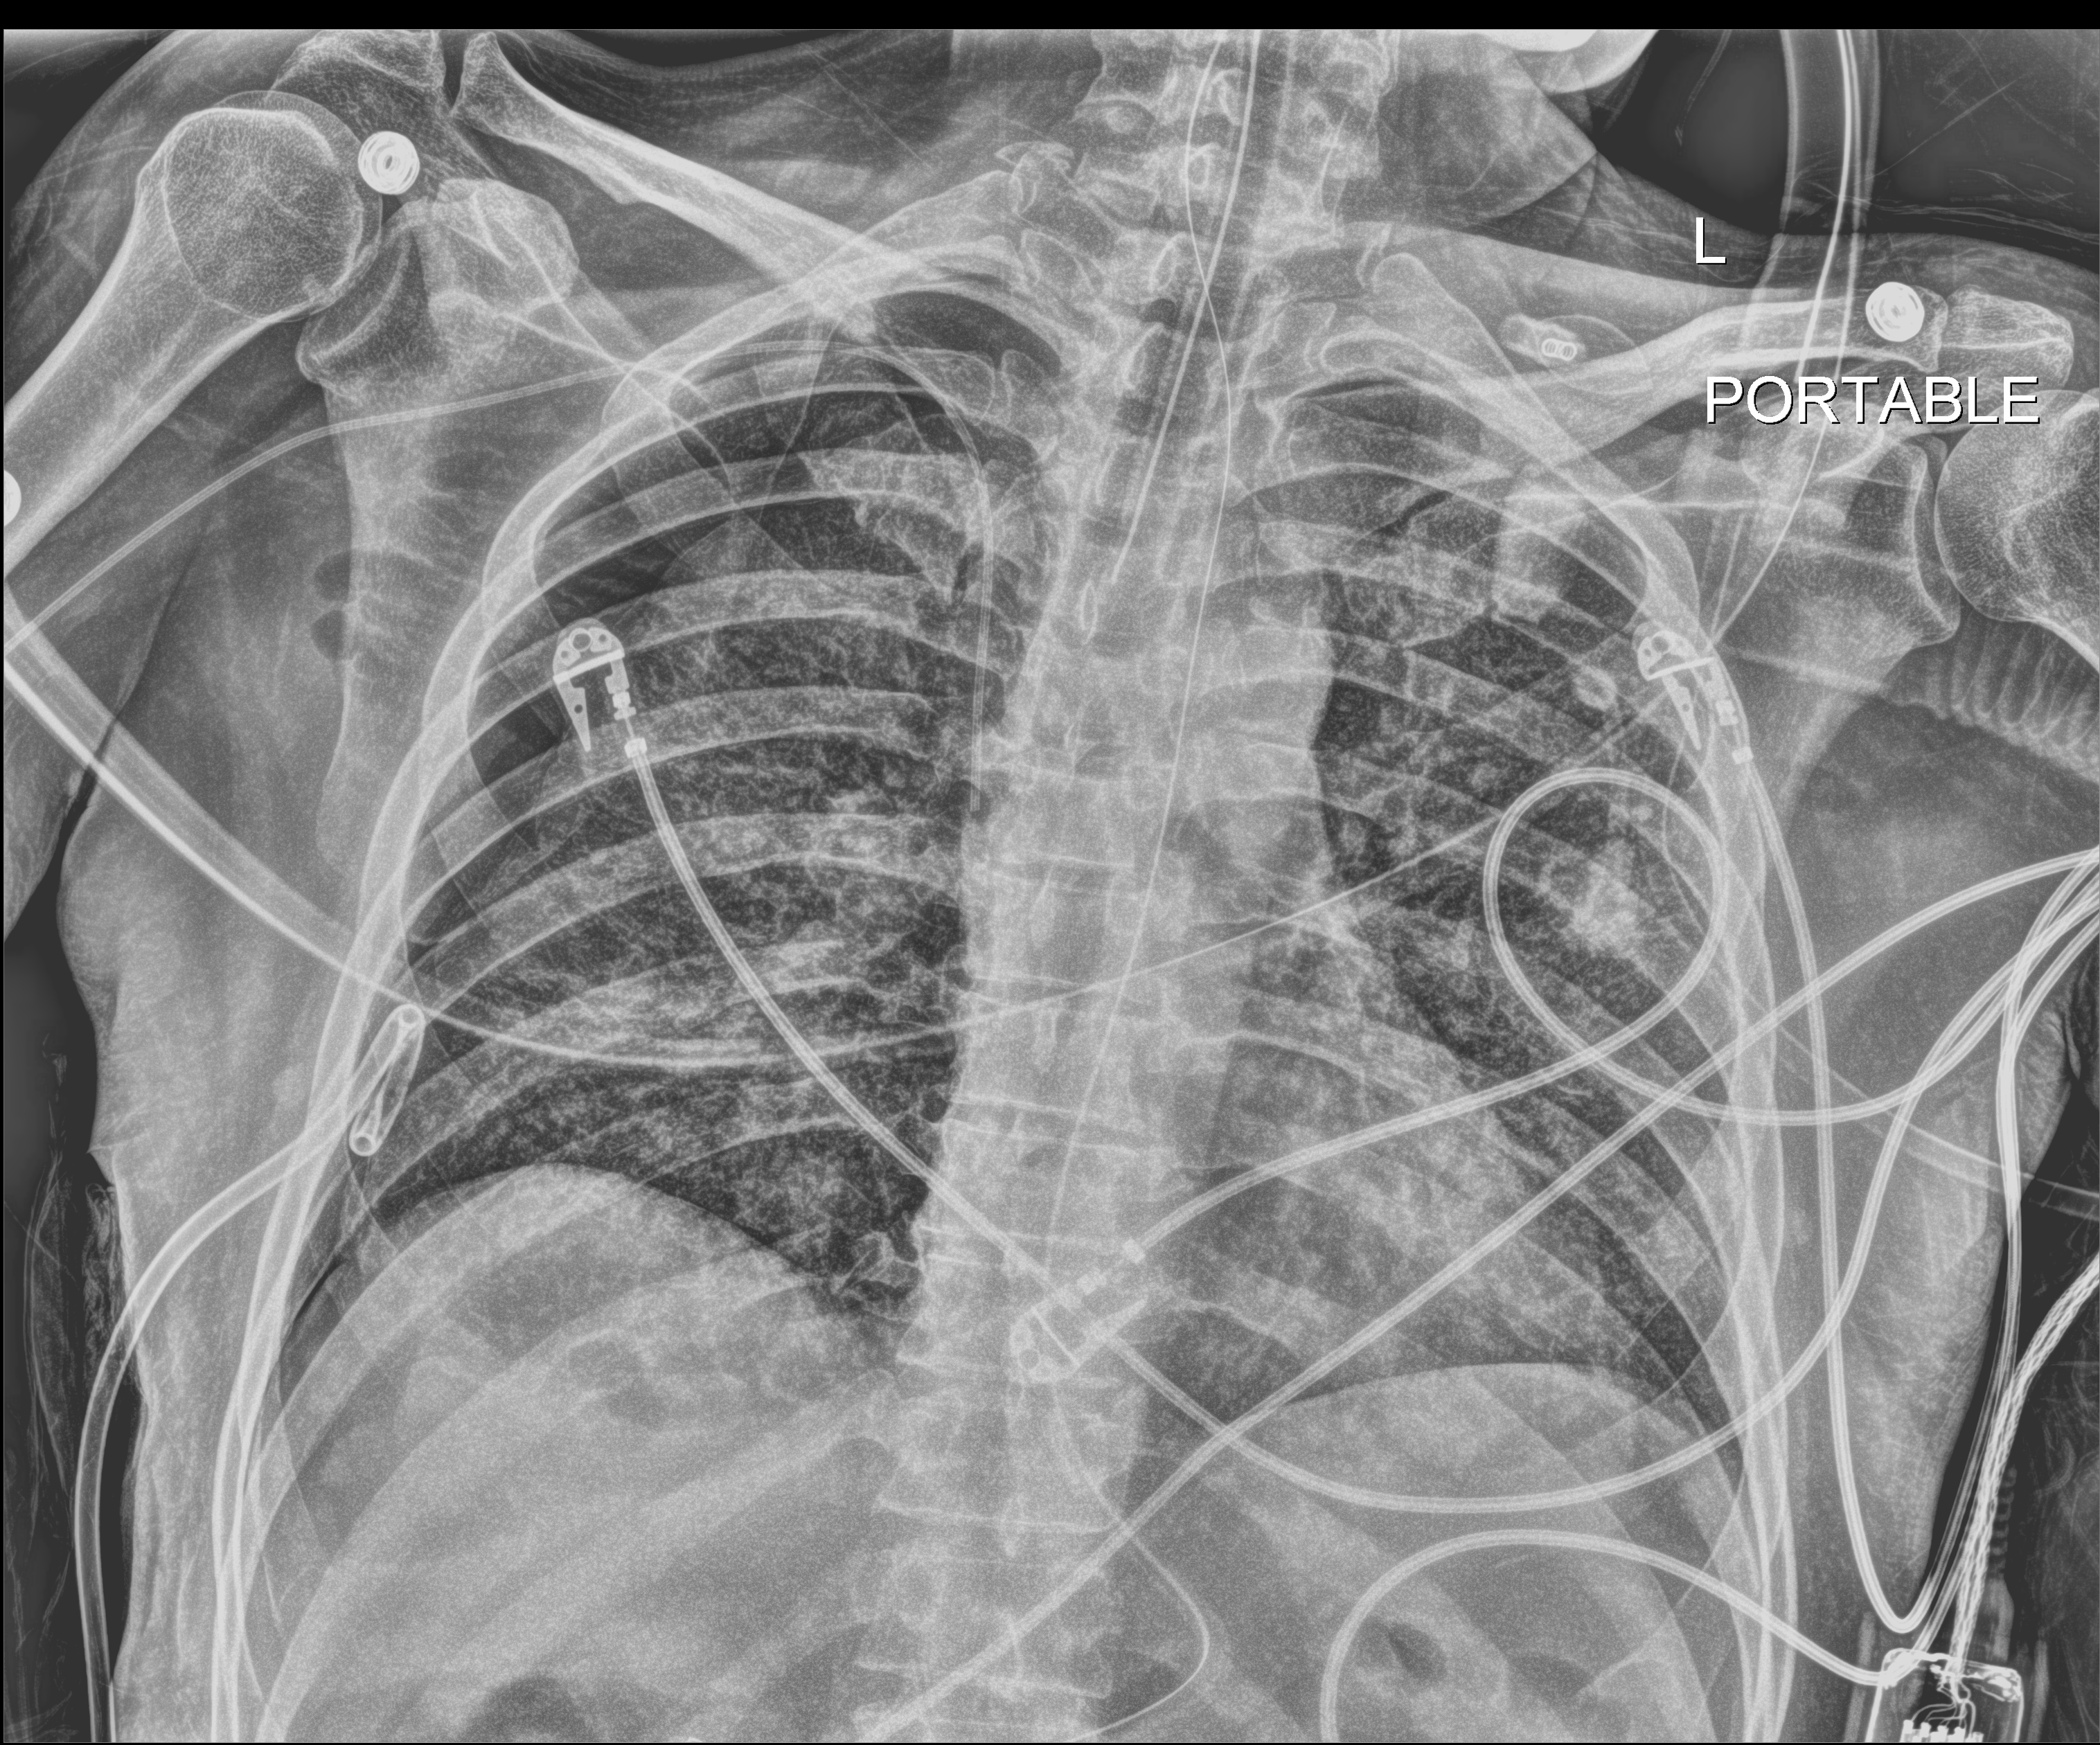
Chest X-ray (portable); anteroposterior (AP) projection. Patient hospitalised with COVID-19; male, aged 18–59 years.
Hospital-stay facts (about this admission, not read from this image; timing relative to this image not recorded): admitted to intensive care during this hospital stay: yes; mechanically ventilated during this hospital stay: yes.